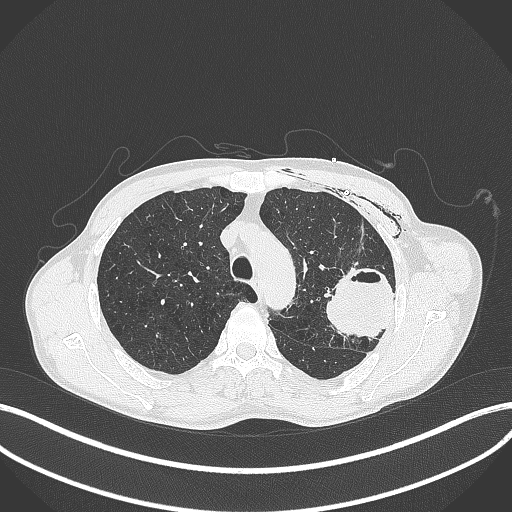
Chest CT, one axial slice; slice 304 of 457 in the series (ordered by position); 120 kVp; lung window (W 1500 / L -600 HU); 1 mm slice thickness; 512 × 512 image matrix, field of view 400 × 400 mm. Male patient, age 58 years. Case-level facts recorded for this patient, not image findings: clinical TNM (as recorded): T3 N0 M0.
Annotated regions visible in this slice (bounding box drawn by a radiologist):
- lung tumour (recorded histology: adenocarcinoma): bounding box (x1, y1, x2, y2) in pixels: (327, 265, 396, 341)